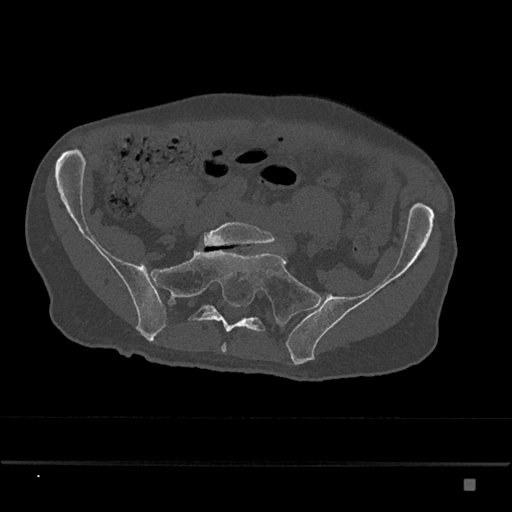
CT including the spine, one axial slice. Position 222 of 797 along the scan axis. Reconstruction kernel Br40s/3. 120 kVp. Bone window (W 1800 / L 400 HU). 0.5 mm slice thickness. 512 × 512 image matrix, field of view 390 × 390 mm. Male patient, age 72 years. Case-level facts recorded for this patient, not image findings: primary cancer: prostate.
Outlined on this slice (semi-automatic segmentation, software-assisted and operator-edited):
- L5 vertebra: bounding box [x1, y1, x2, y2] px = [203, 222, 276, 246]